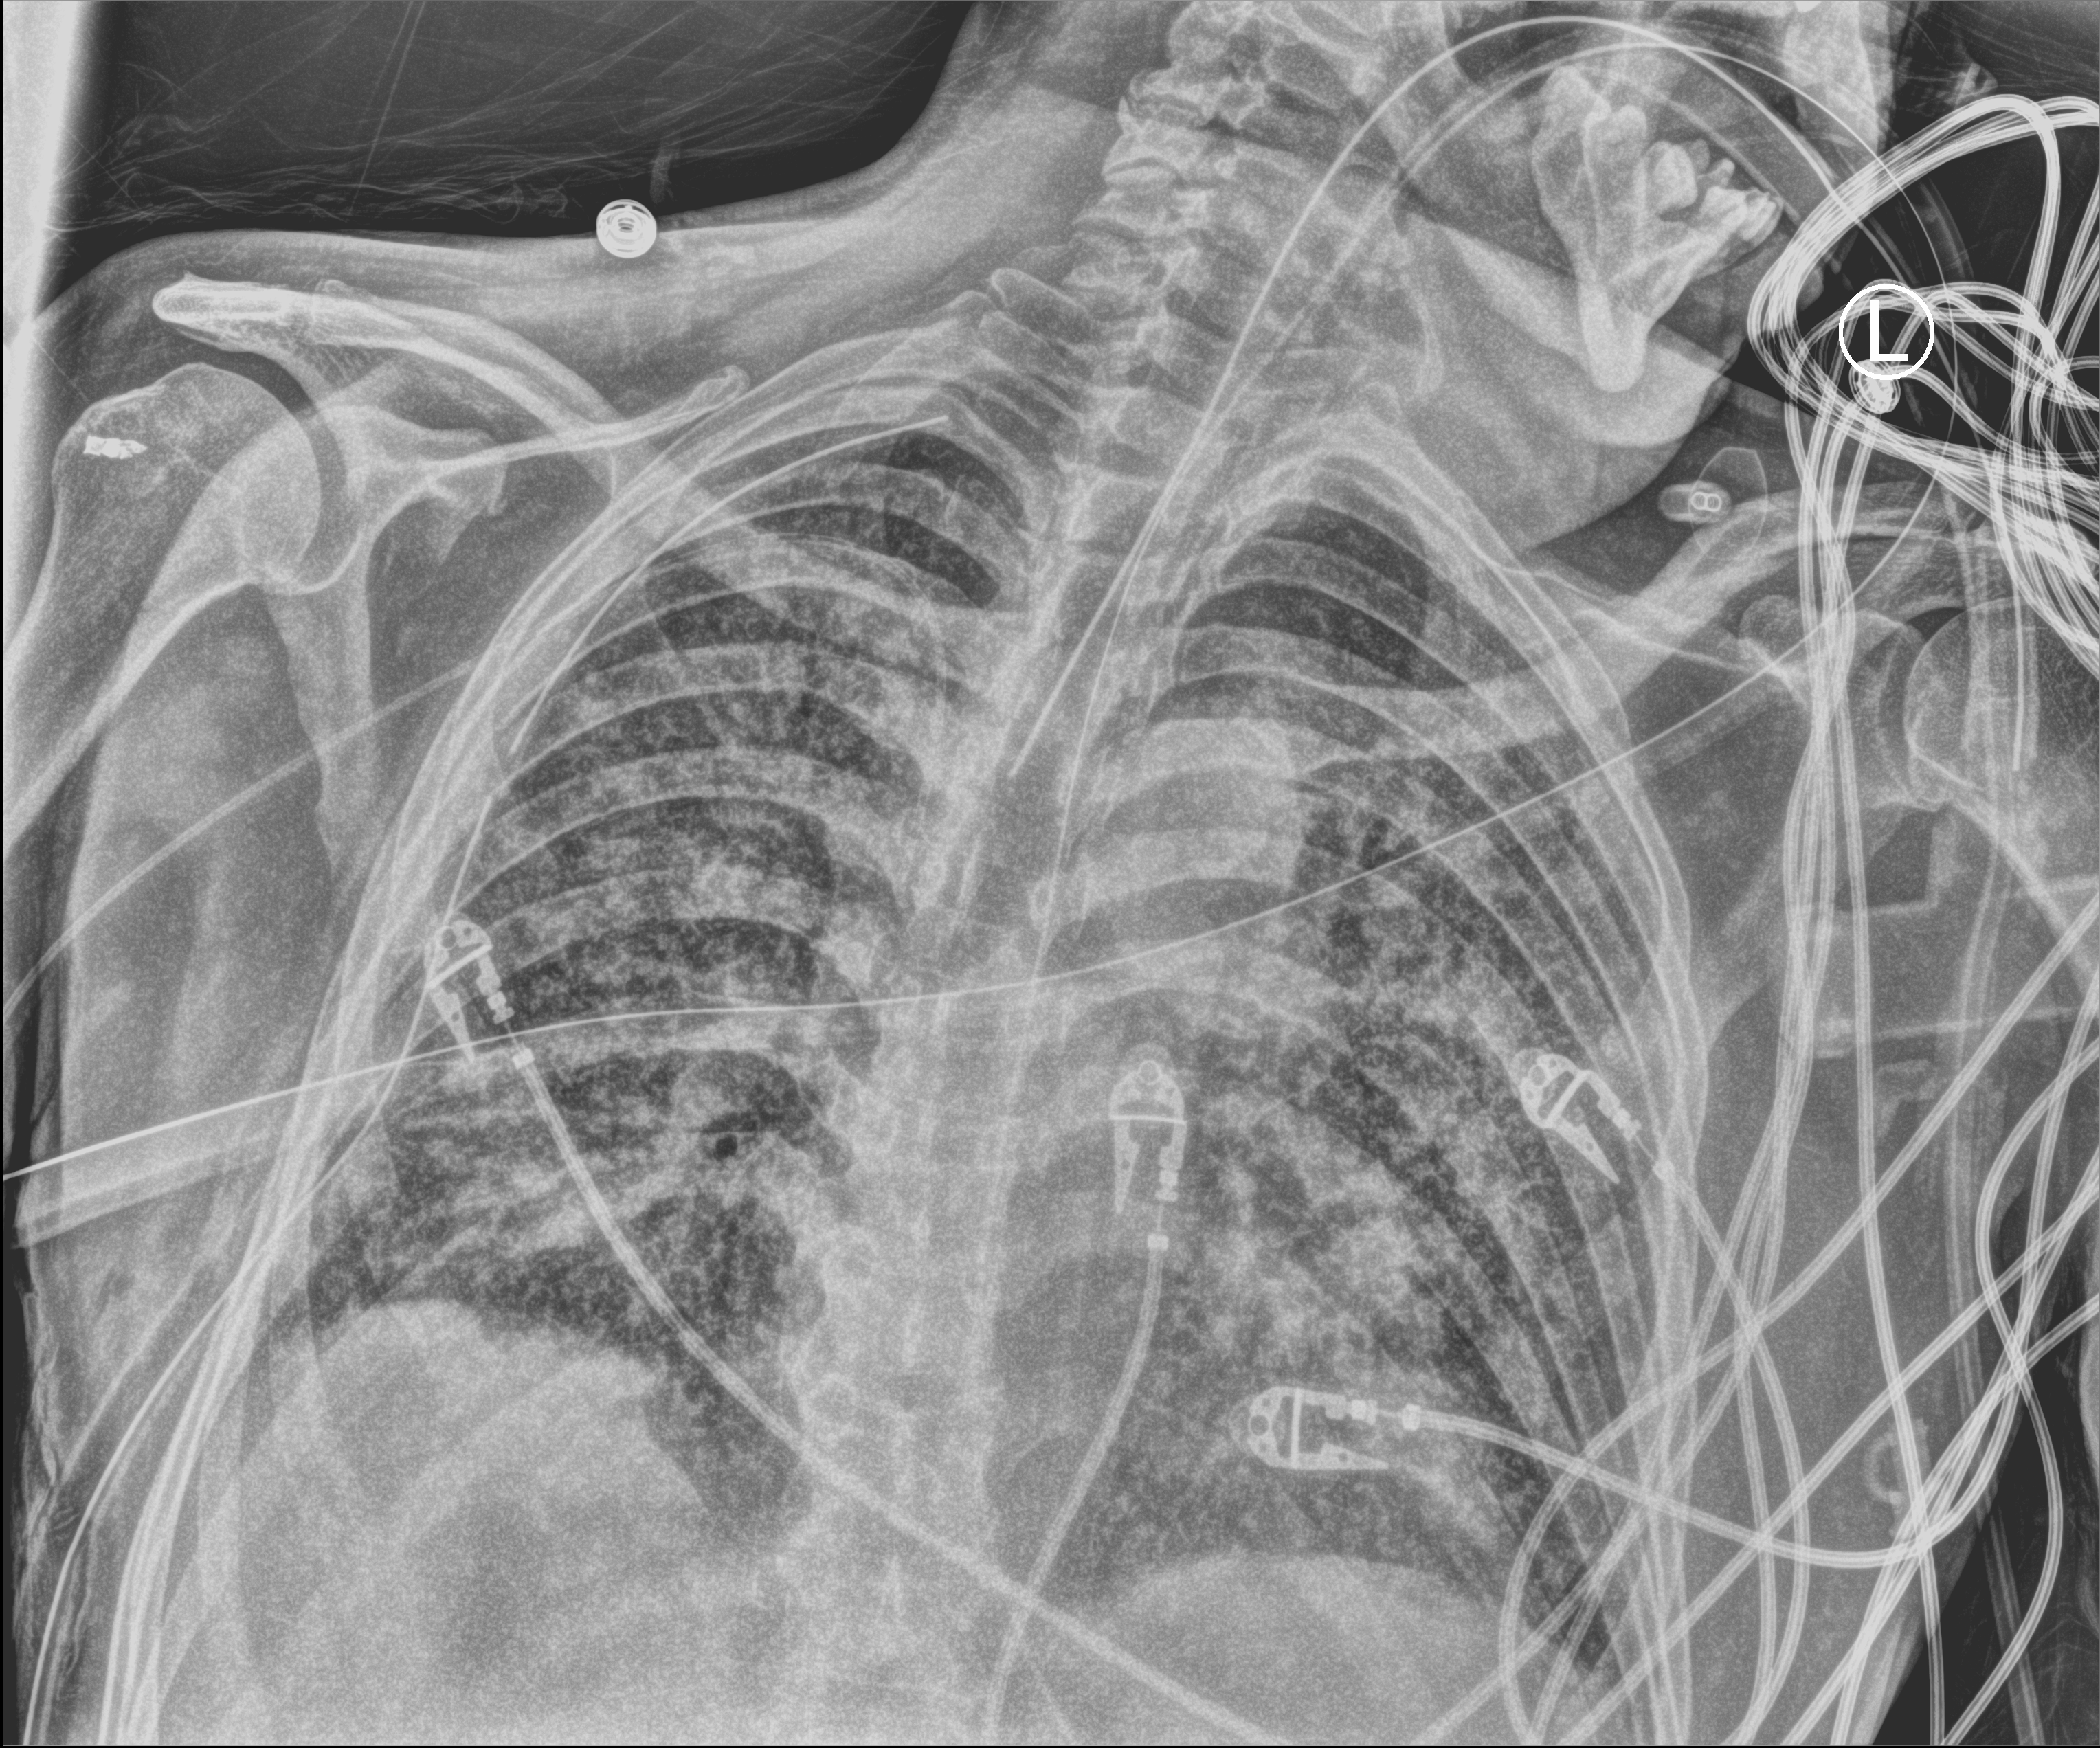
Portable chest radiograph. Patient hospitalised with COVID-19; male, aged 60–74 years.
From the hospital-stay record, not from the radiograph (when in the stay this image was taken is not recorded):
- length of hospital stay: 65 days
- admitted to intensive care during this hospital stay: yes
- diabetes (admission record): no